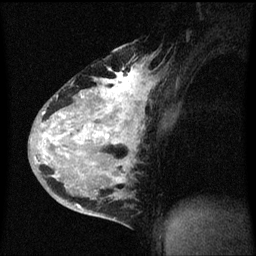
Breast MRI (dynamic contrast-enhanced), one sagittal slice. Position 40 of 60 along the scan axis. Dynamic contrast-enhanced series, image 2 of 3 at this slice position (ordered by acquisition). 1.5 T. TE 4.2 ms, TR 8.4 ms. 256 × 256 image matrix, field of view 200 × 200 mm. Female patient, age 34 years. Case-level facts recorded for this patient, not image findings: setting: breast cancer imaged before/during neoadjuvant chemotherapy; receptor status: HR-positive, HER2-negative.
Outlined on this slice (semi-automatic segmentation, software-assisted and operator-edited):
- analysis volume of interest (the breast-tissue region the enhancement analysis was run in; not a lesion): bounding box <34,48,157,215> (left, top, right, bottom; pixels)
- tumour enhancement mask (voxels above the 70 % enhancement threshold inside the analysis volume of interest): <42,68,143,209>